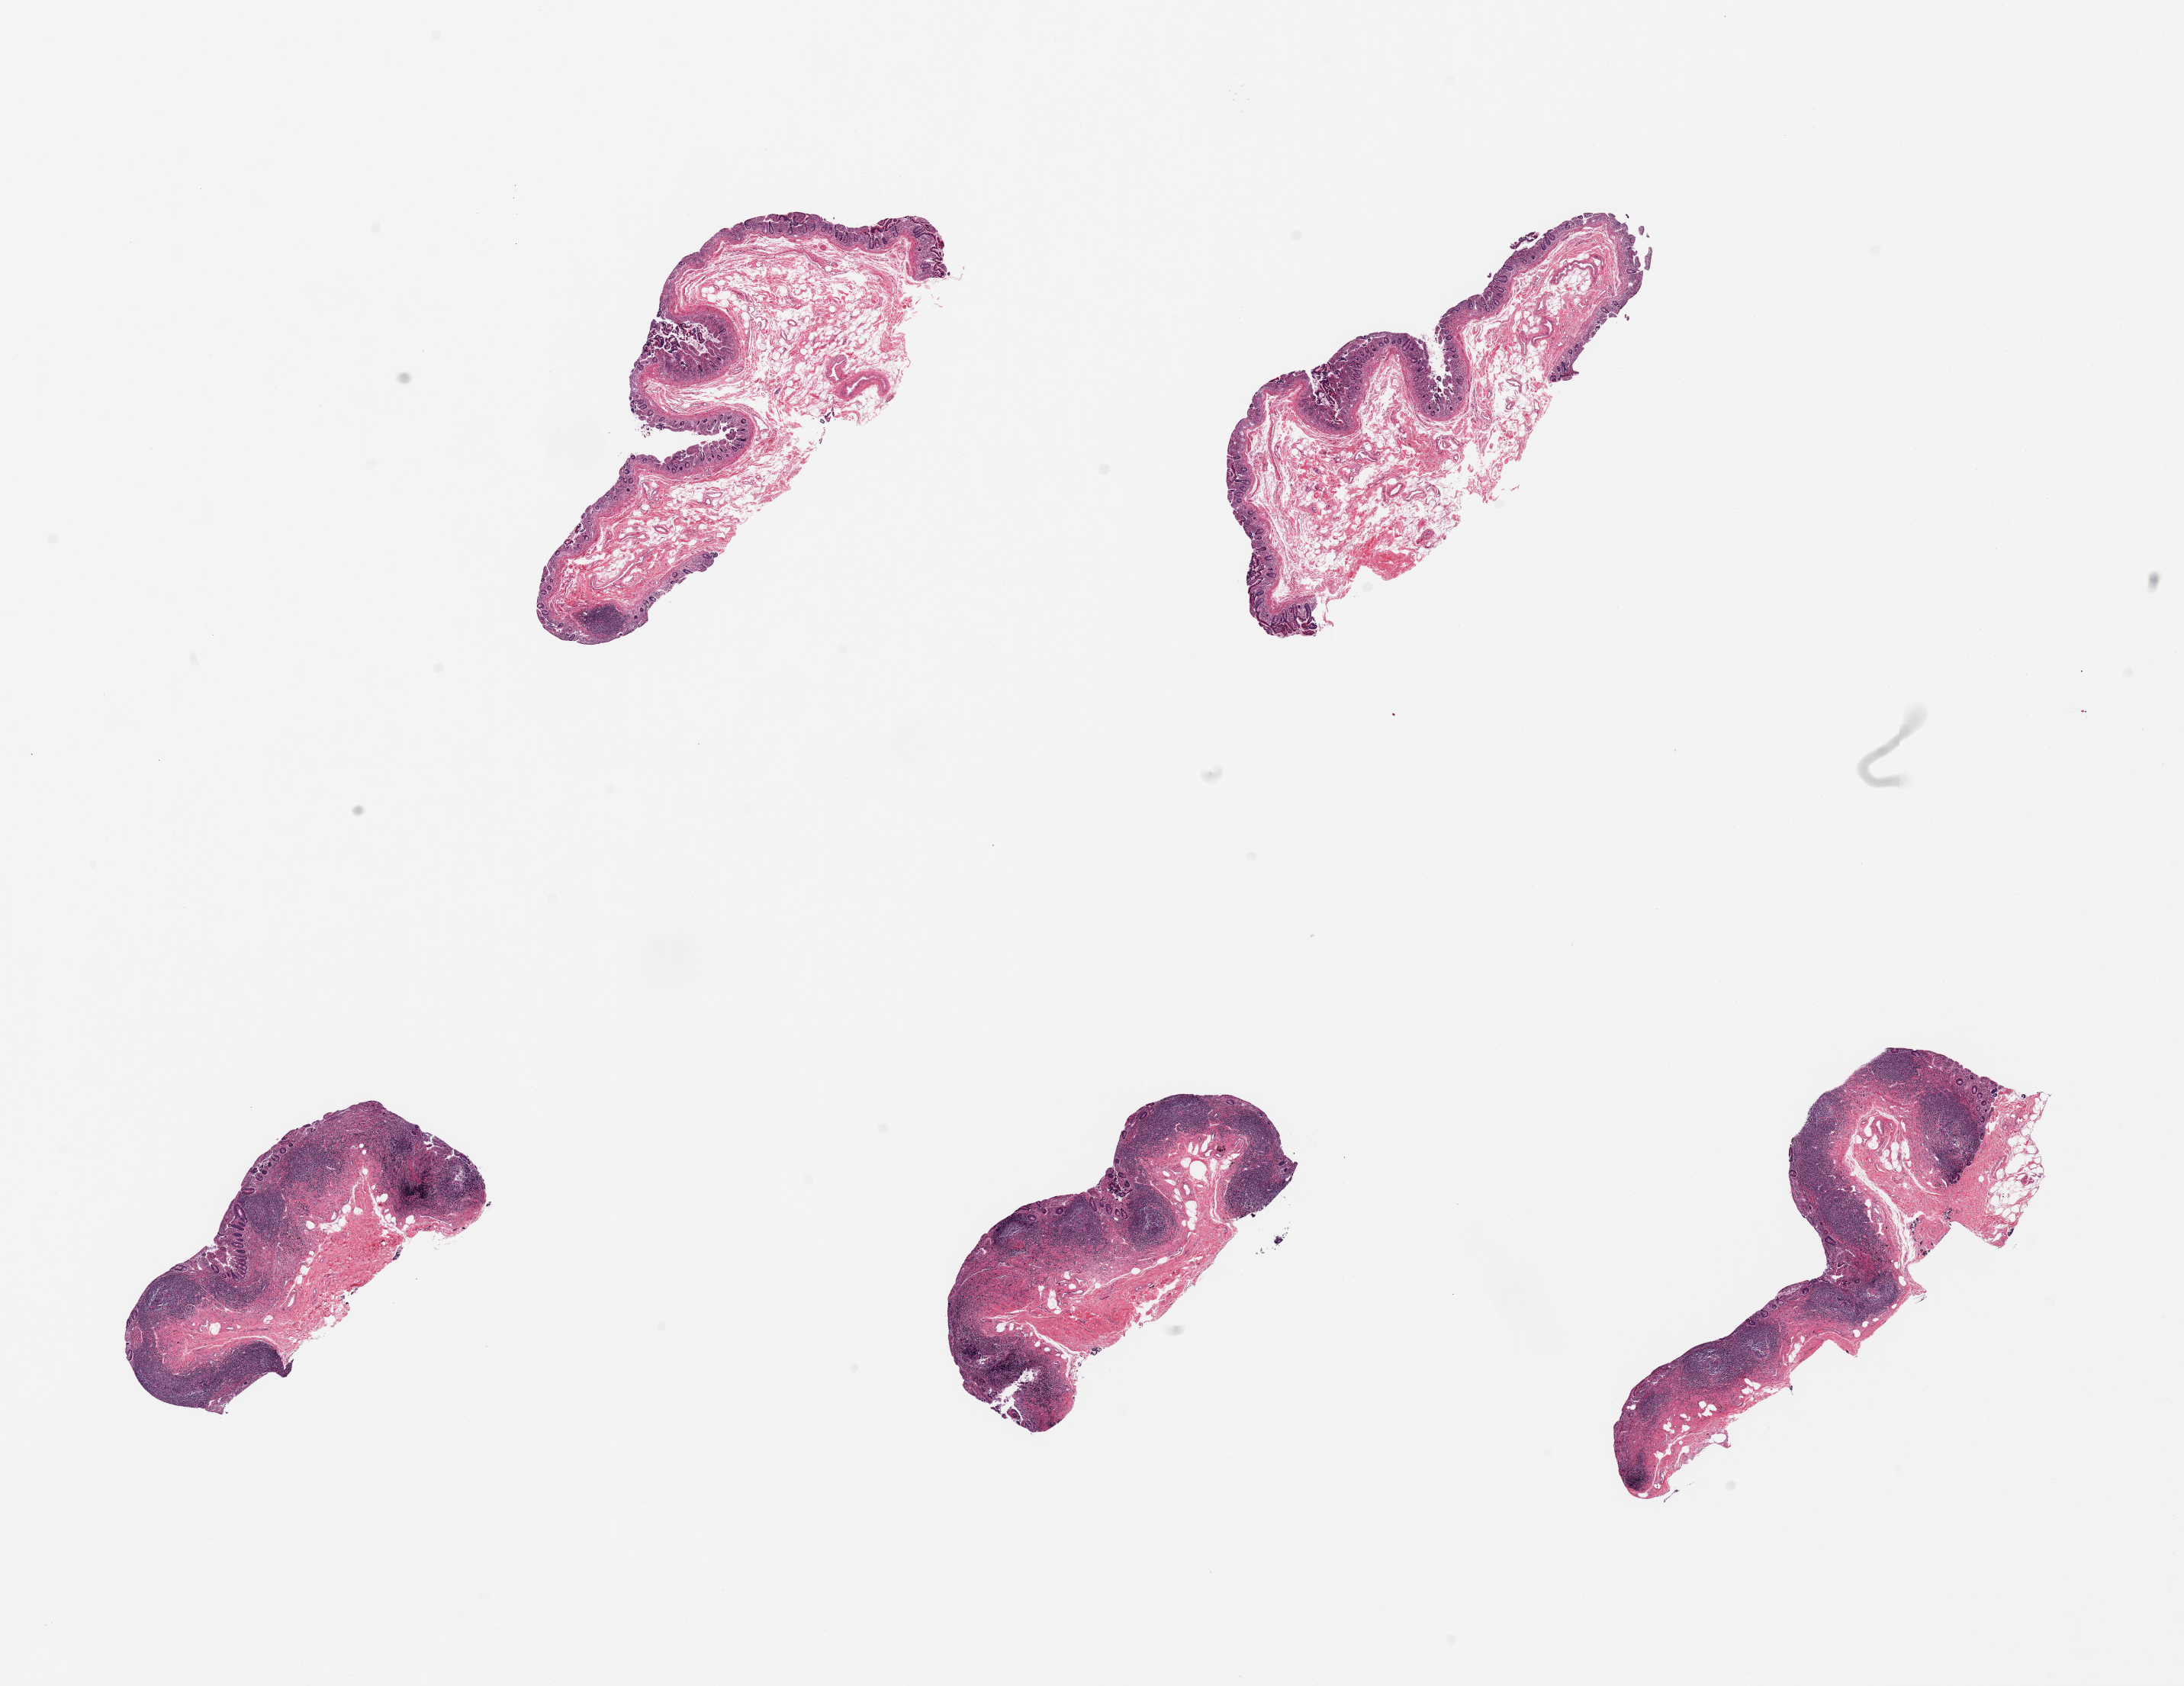
Whole-slide image, H&E stain, brightfield — a low-resolution overview of the entire scanned area, about 22.6 x 17.5 mm (acquisition: 20x scan); PAXgene-fixed paraffin-embedded (PFPE) section; section of ileum (target tissue); tissue donor sample.
Pathologist's review note for this sample: 5 pieces; abundant lymphoid tissue in 3 pieces.